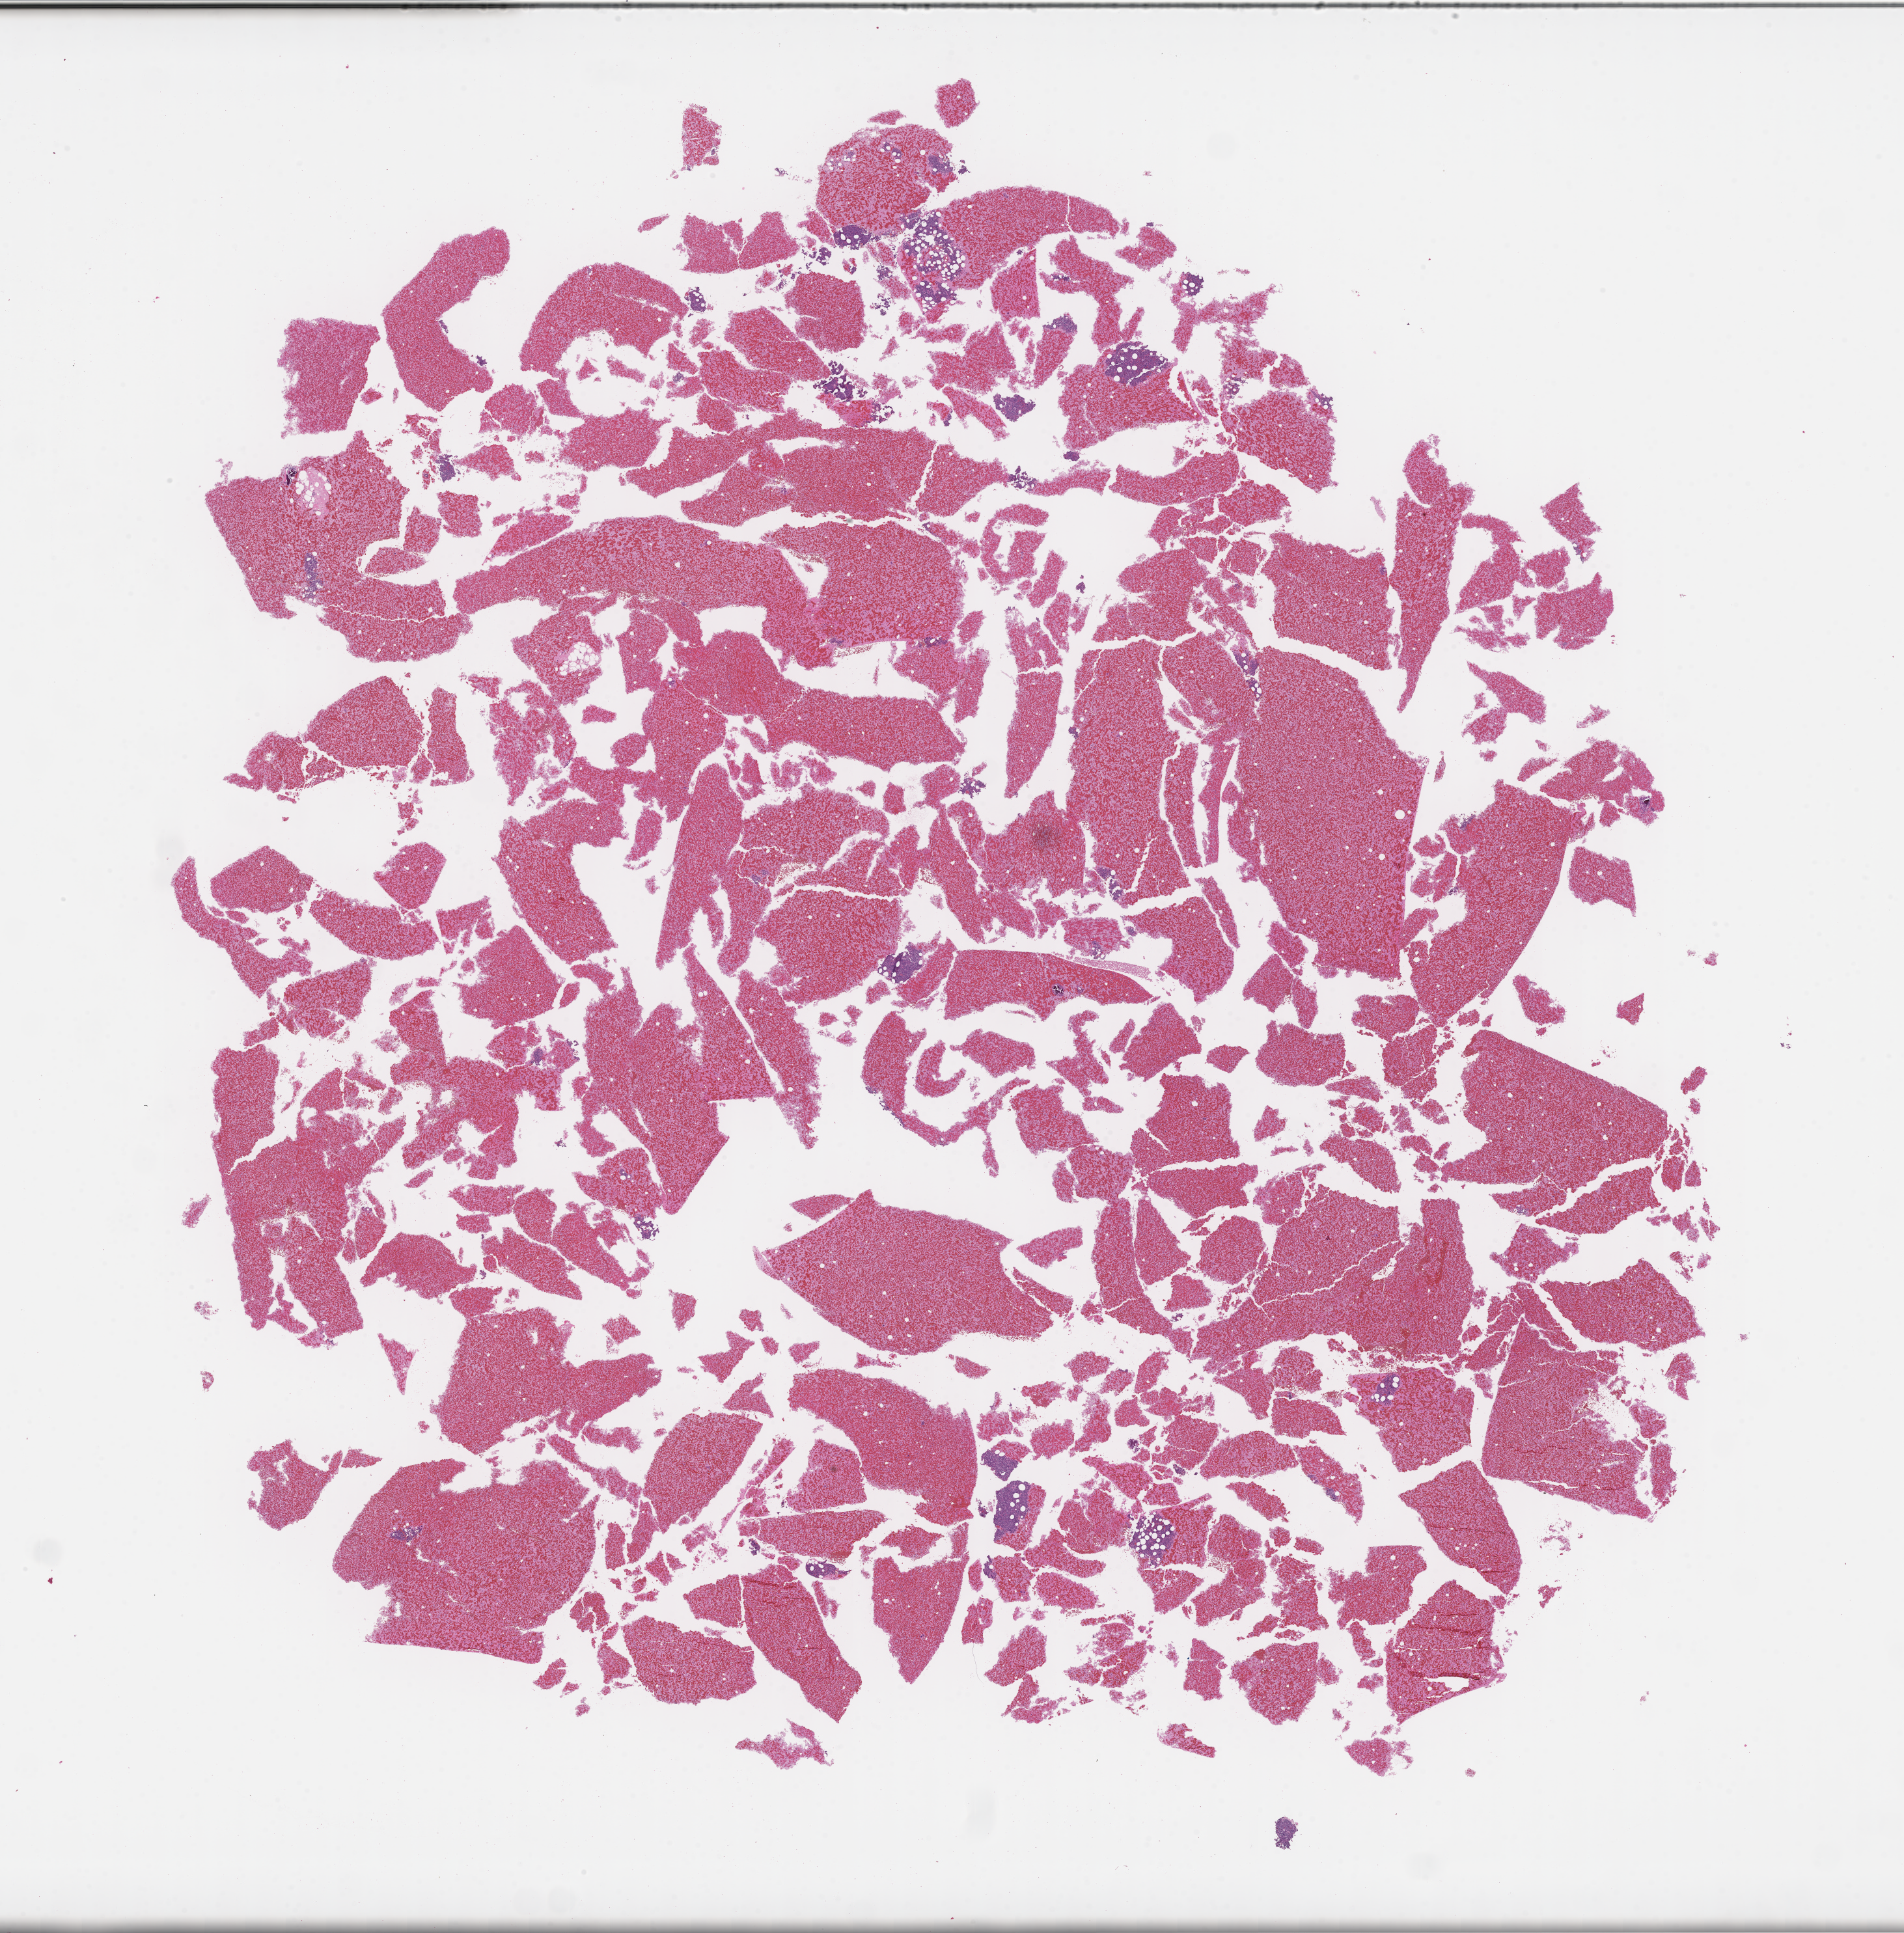
Digitized H&E-stained section, shown as a low-resolution overview of the whole scanned area (about 23.6 x 24.0 mm); FFPE section; site: bone marrow; archival tissue. Female patient.
This section: primary tumor. Diagnosis: Plasma Cell Myeloma.